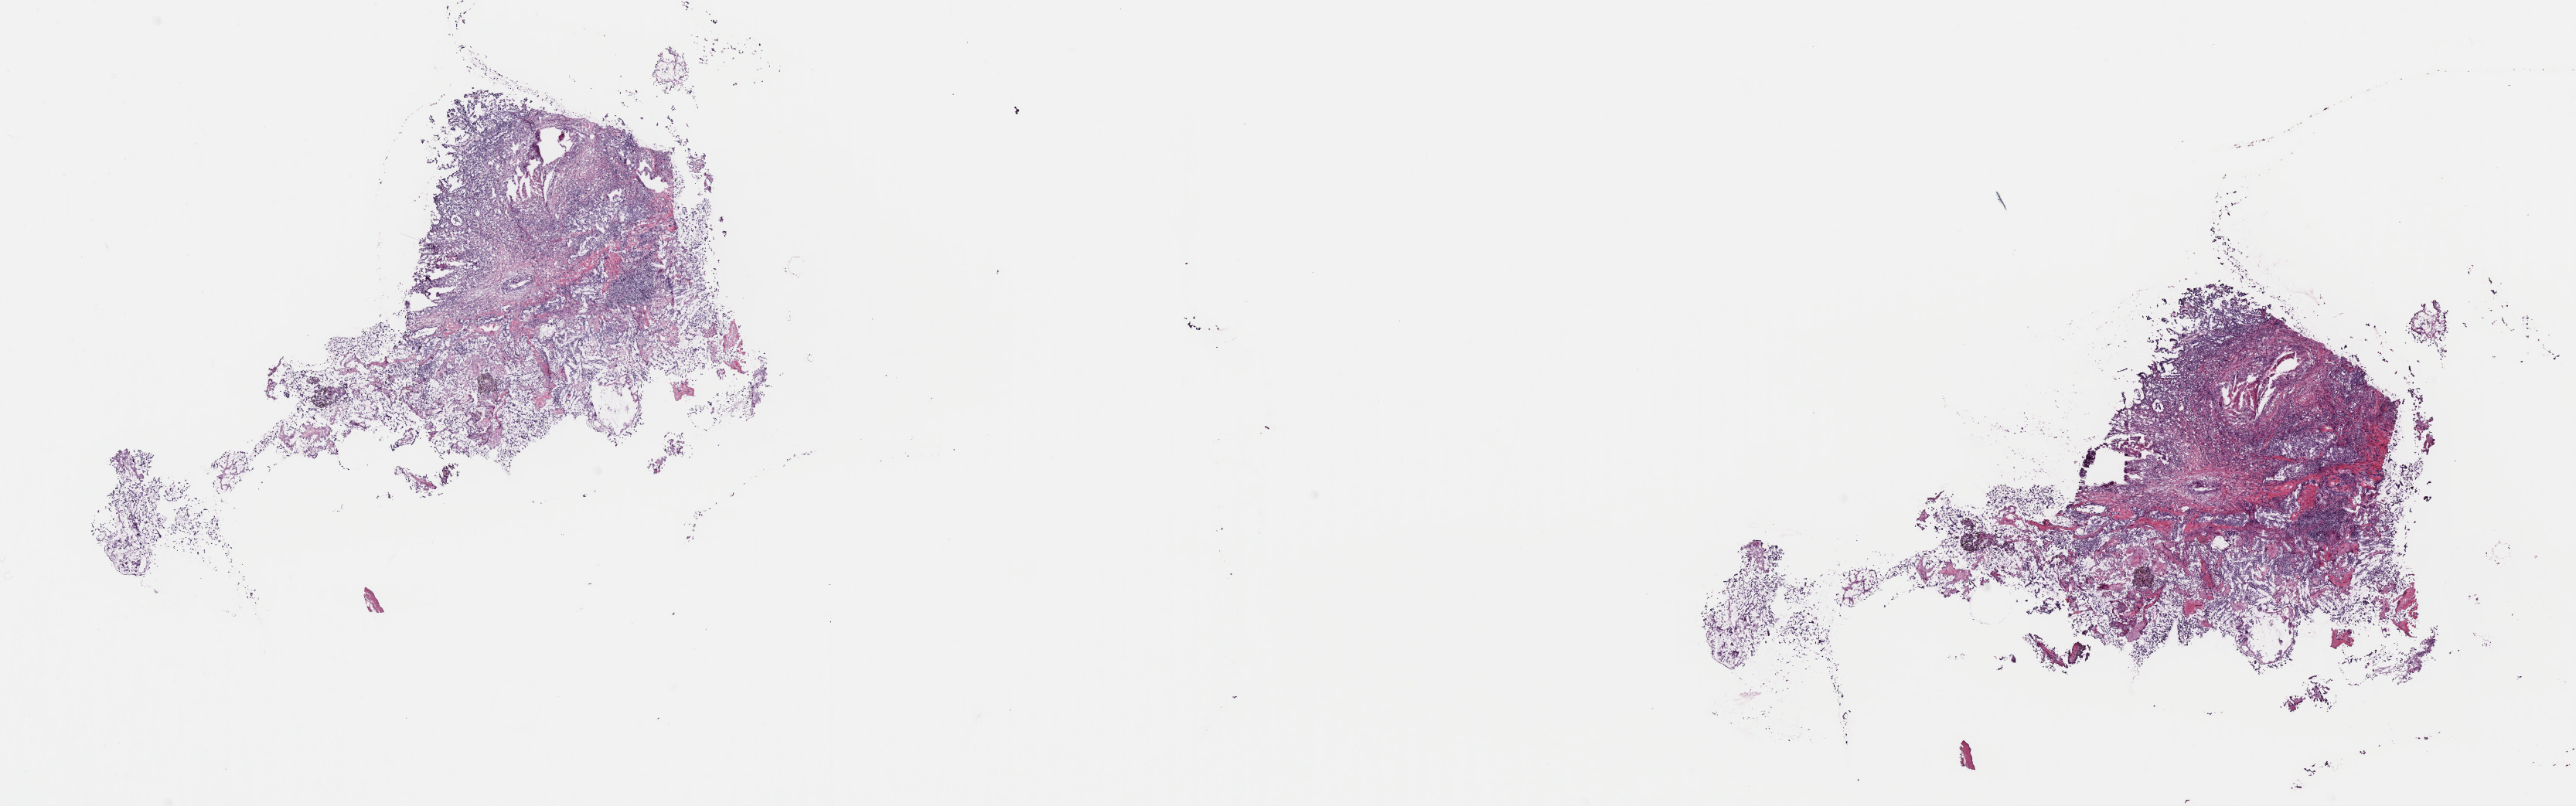
Whole-slide histology image, H&E — a low-resolution overview of the entire scanned area, about 26.3 x 8.2 mm. Frozen section. Sample: primary tumour, thyroid. Male patient; age at initial diagnosis 42 years. Pathologist review of this section (percent, as recorded): tumour cells 95%, tumour nuclei 80%, normal cells 0%, stromal cells 0%, necrosis 5%. Infiltration values recorded for this section: lymphocyte infiltration 5%, monocyte infiltration 1%, neutrophil infiltration 1%.
Histologic diagnosis: Papillary adenocarcinoma, NOS. AJCC pathologic stage: I (6th edition).